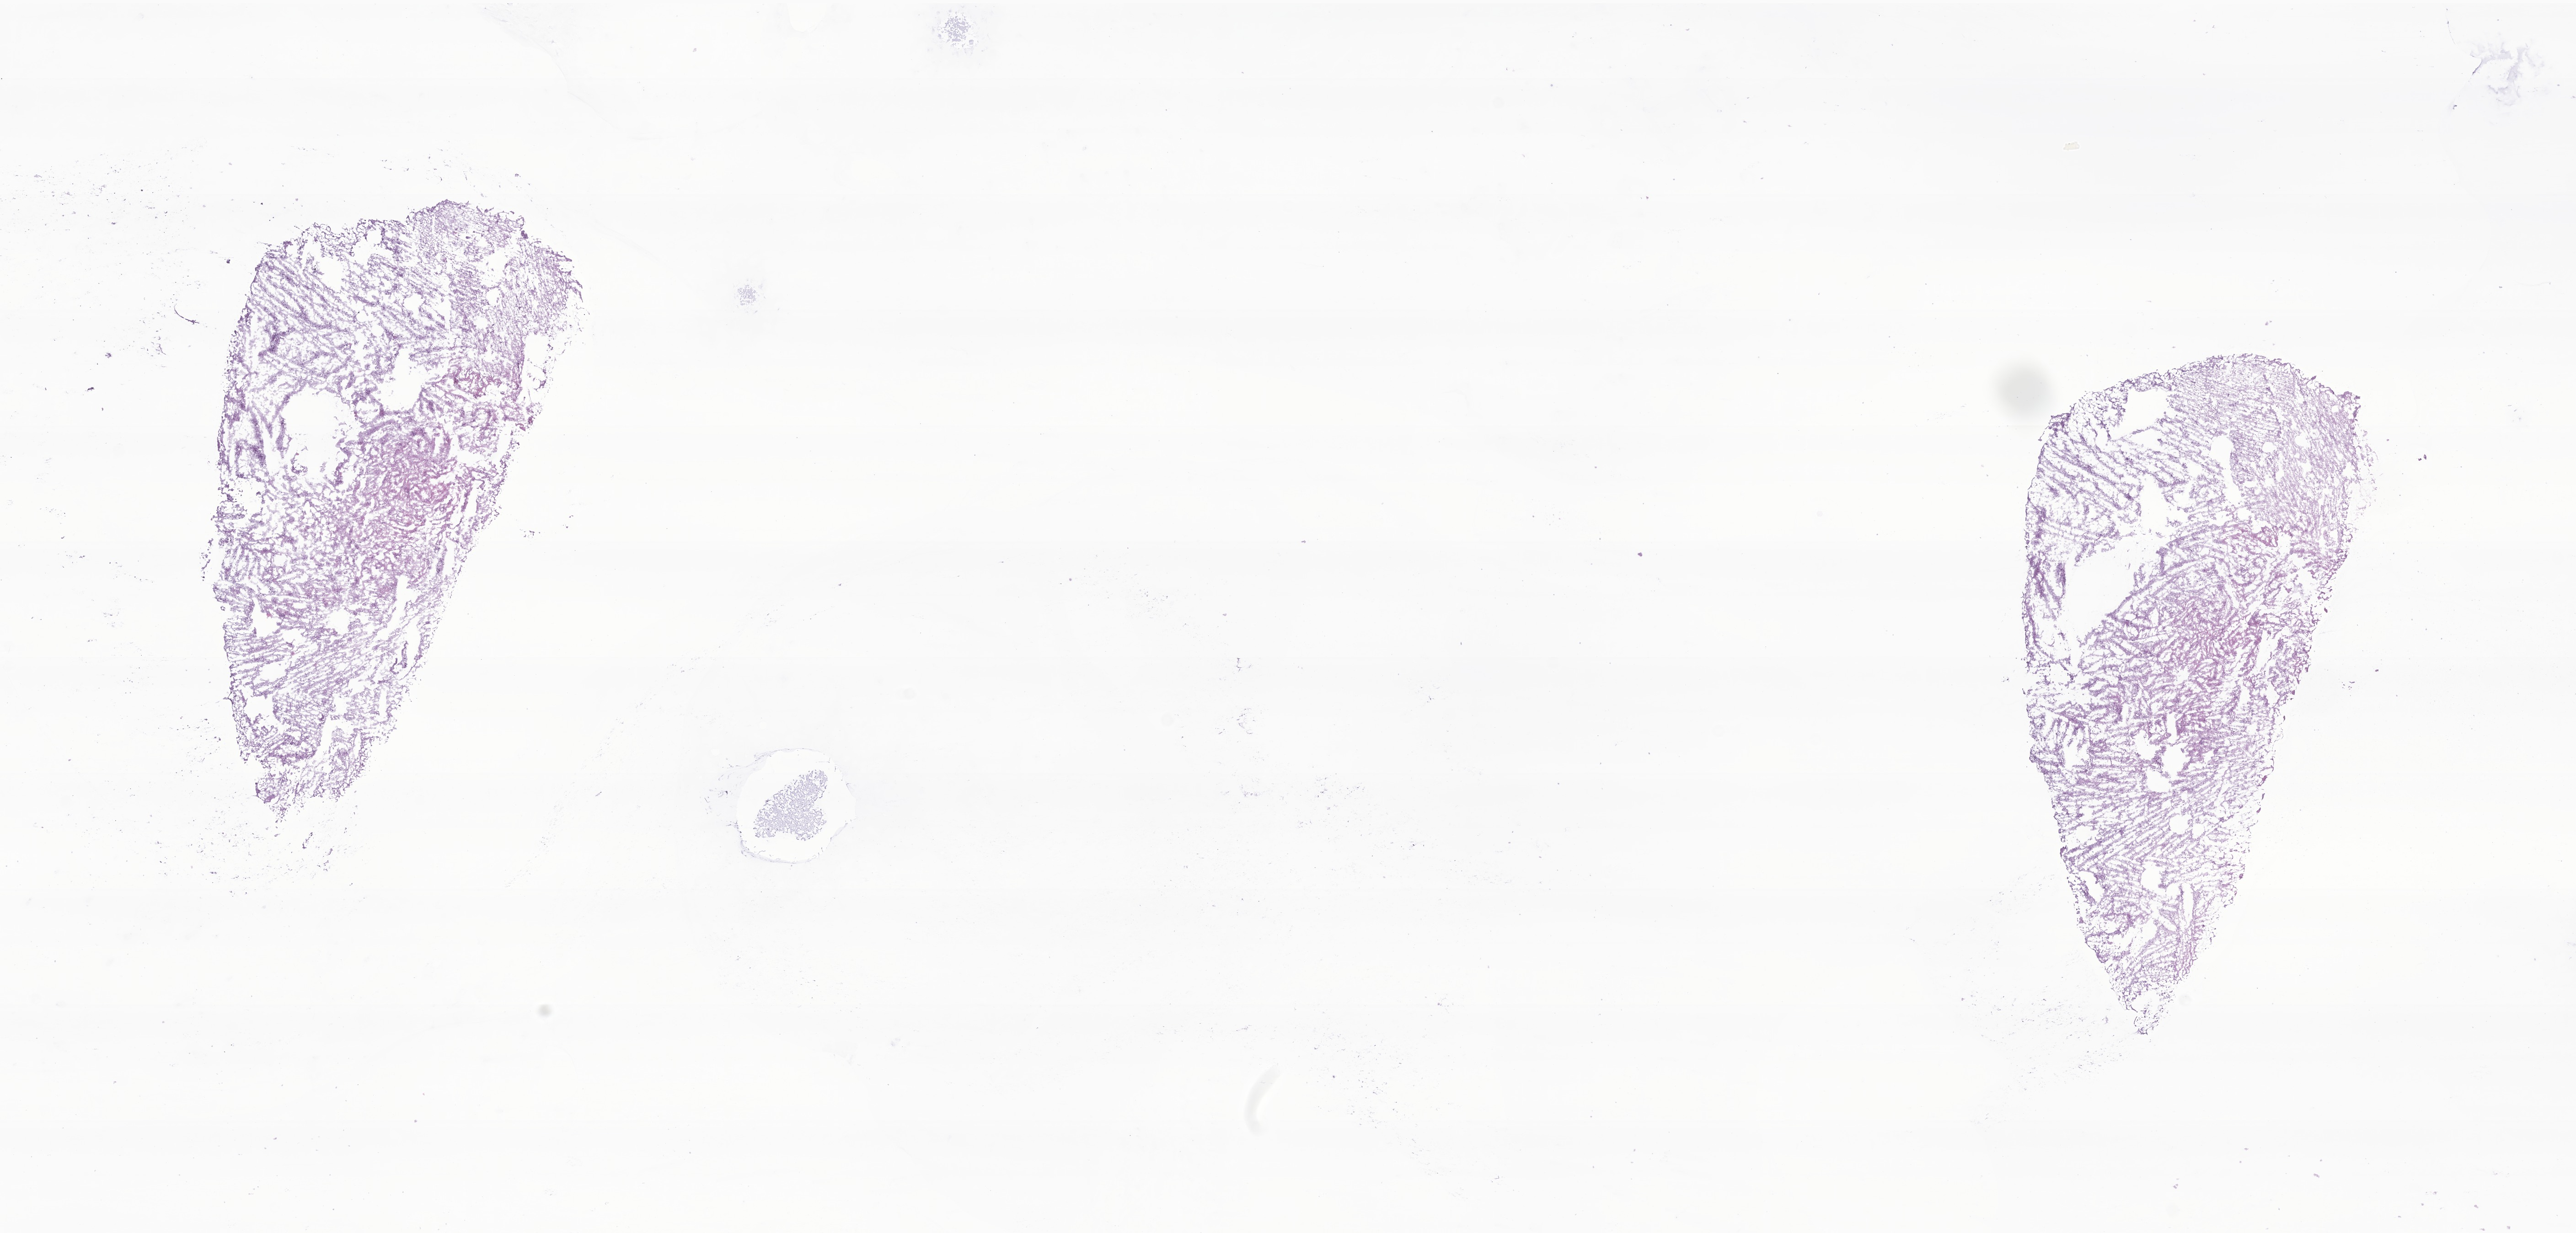
Haematoxylin and eosin whole-slide image of tumor tissue from the brain, whole scanned area (about 23.7 x 11.4 mm) shown as a low-resolution overview, cryosection (OCT / tissue freezing medium). Patient: male, age 48 months.
- diagnosis: Pilocytic astrocytoma